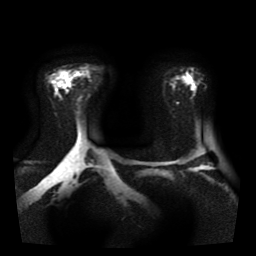
Breast MRI, one axial slice; slice 27 of 41 in the series (ordered by position); diffusion-weighted series; image 2 of 4 stored at this slice position (different b-values; order by instance number); 1.5 T; 5 mm slice thickness; 256 × 256 image matrix, field of view 330 × 330 mm. Female patient.
Outlined on this slice (manually delineated by an expert):
- tumour on diffusion-weighted imaging: box from (x=66, y=79) to (x=70, y=84) px